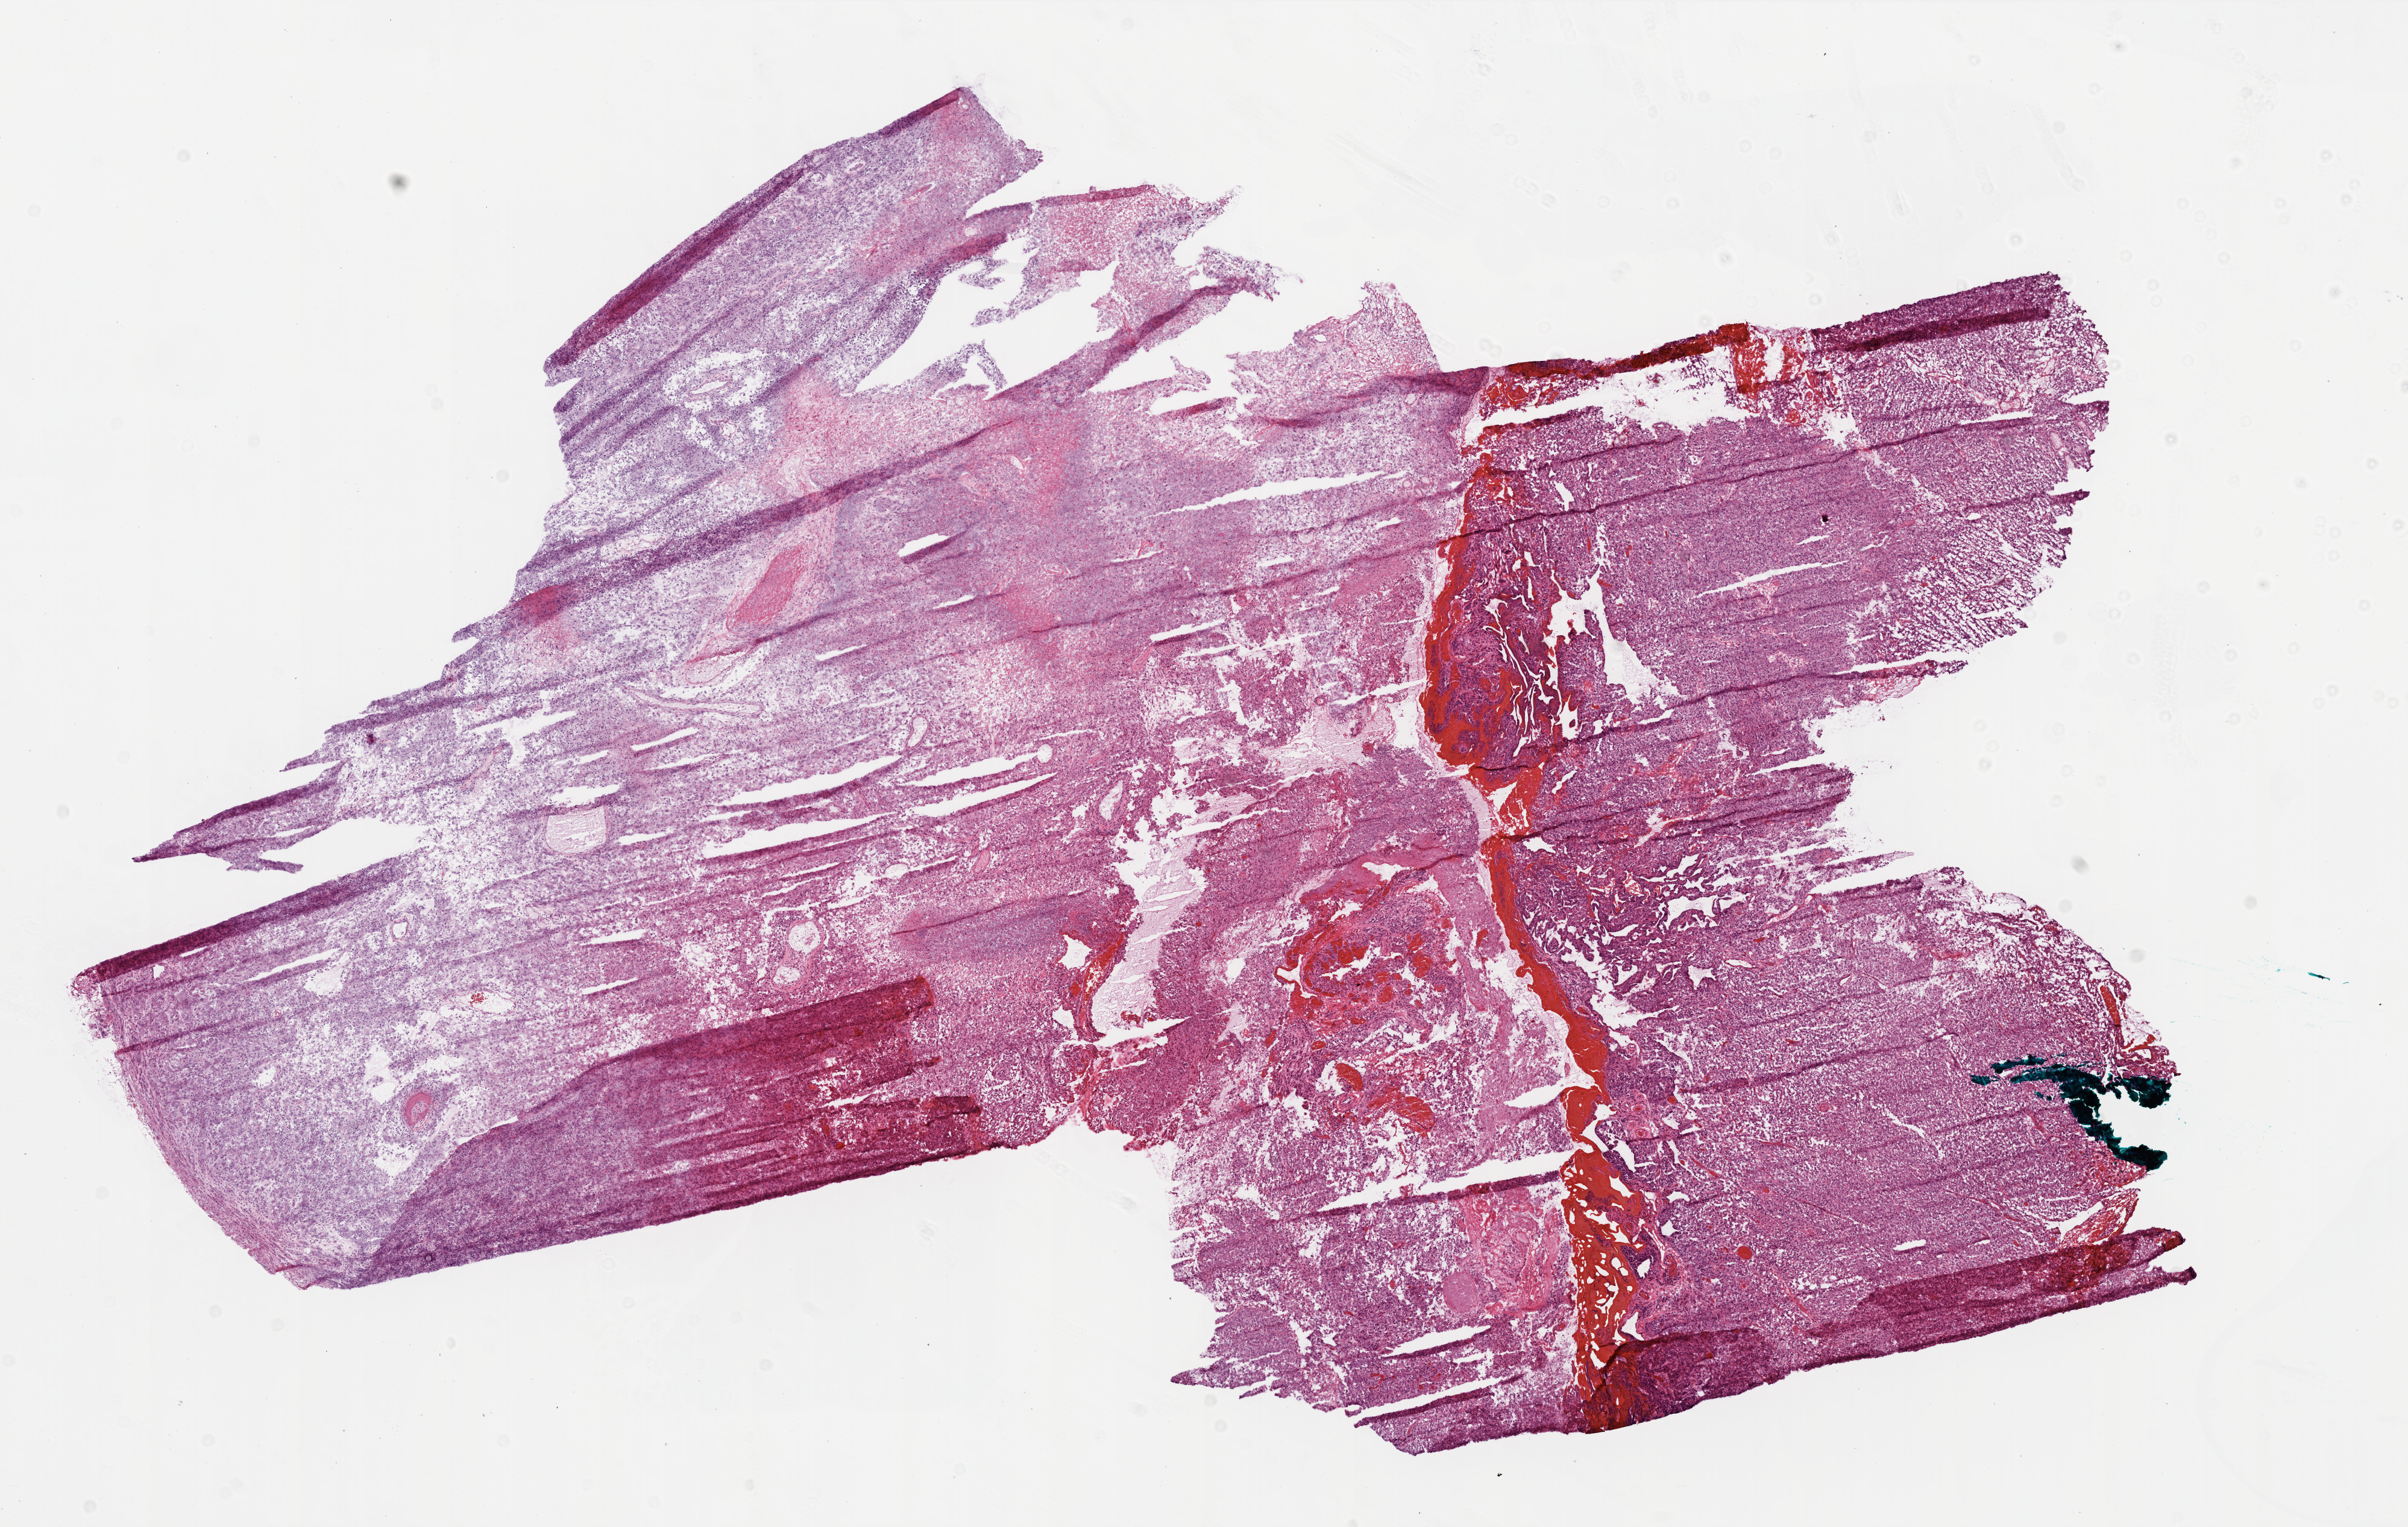
Whole-slide histology image, Hematoxylin and eosin (H&E) stained, whole scanned area (about 16.0 x 10.1 mm, acquisition: 20x scan) shown as a low-resolution overview, frozen section from the bottom of the tissue portion, brain, primary tumour sample. Male patient; age at initial diagnosis 54 years. Pathologist review of this section (percent, as recorded): tumour cells 75%, tumour nuclei 85%, stromal cells 5%, necrosis 20%.
Histologic diagnosis: Glioblastoma.